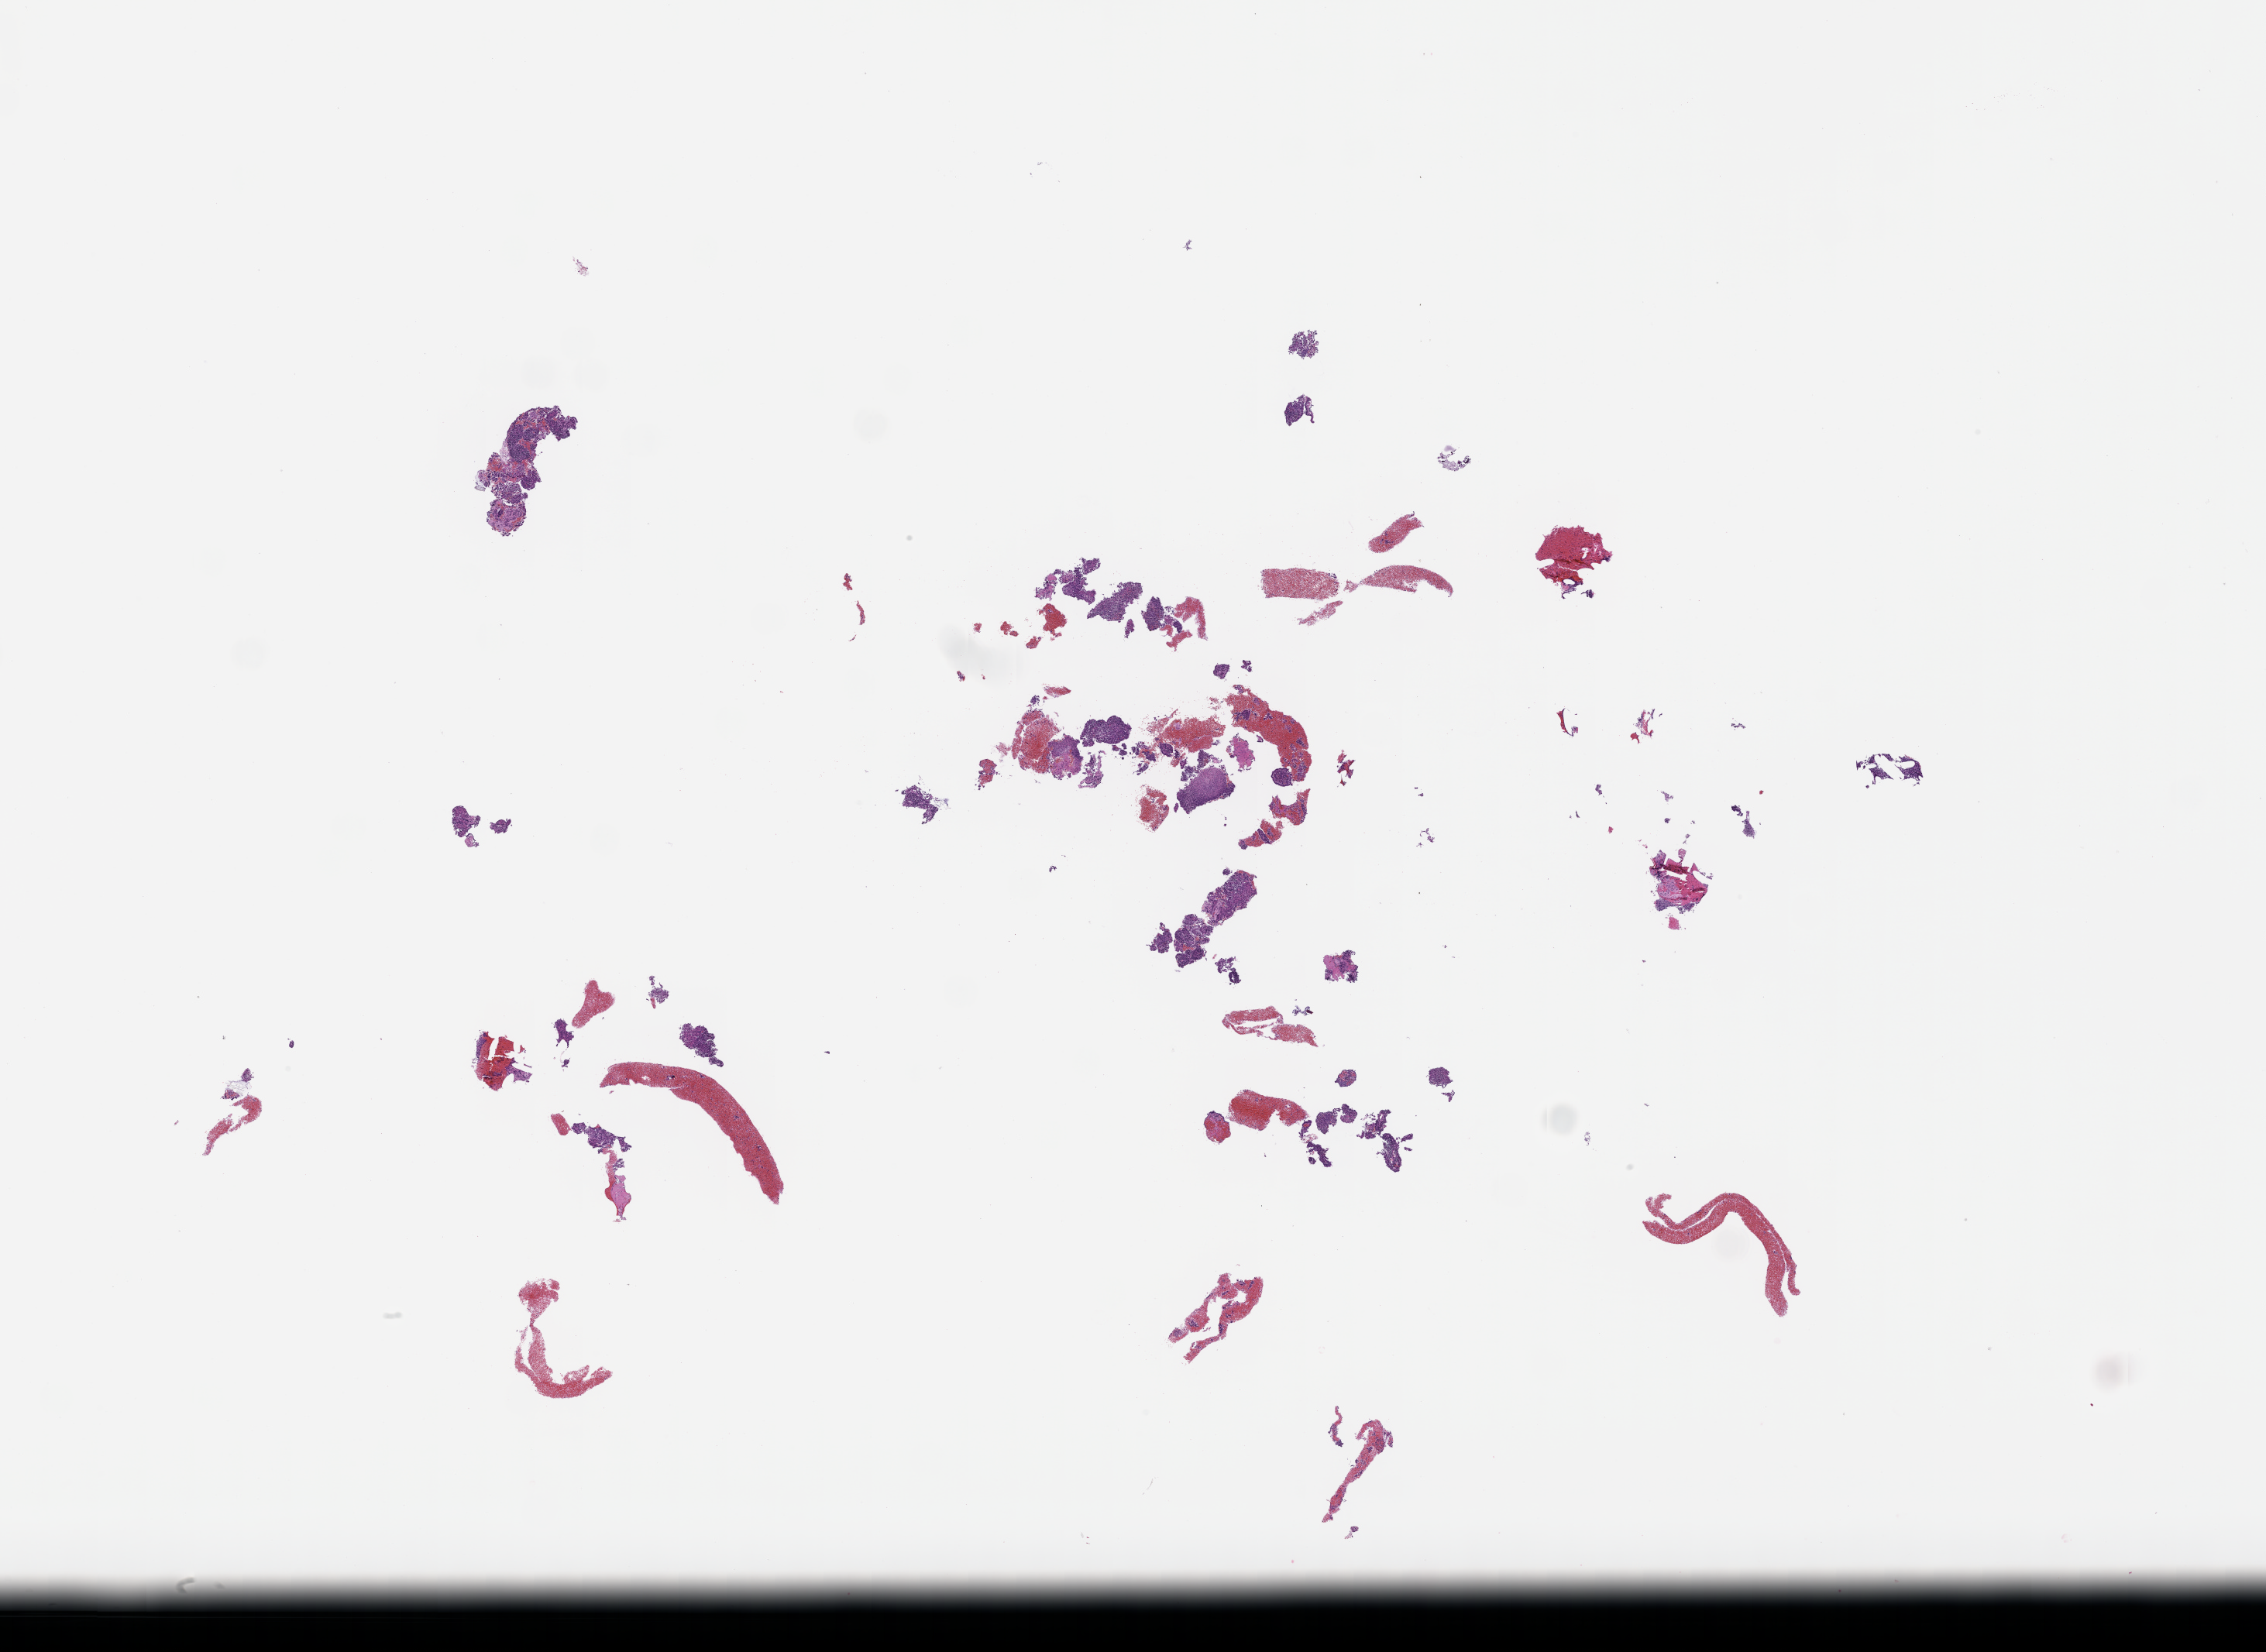
H&E whole-slide image — low-resolution overview of the scanned area, about 23.6 x 17.2 mm; formalin-fixed paraffin-embedded section; site: lung; collected on treatment. Male patient.
This section: primary tumour tissue. Diagnosis: Non-Small Cell Lung Carcinoma.